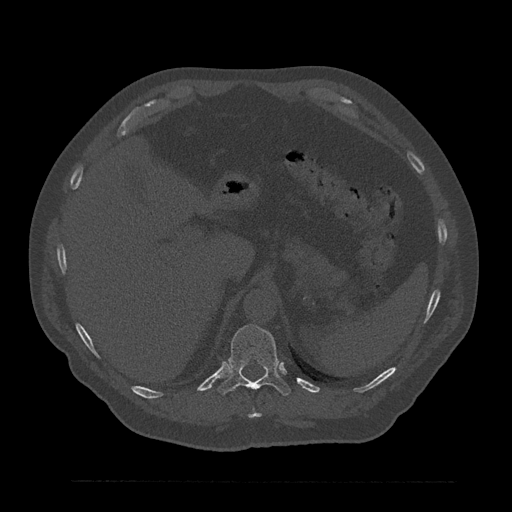
CT including the spine, one axial slice; position 301 of 797 along the scan axis; reconstruction kernel Br40s/3; 120 kVp; bone window (W 1800 / L 400 HU); 0.5 mm slice thickness; 512 × 512 image matrix, field of view 430 × 430 mm. Patient: male, 61 years. Case-level facts recorded for this patient, not image findings: primary cancer: prostate.
Structures marked on this image (semi-automatically segmented with operator editing):
- T10 vertebra: box from (x=248, y=409) to (x=261, y=418) px
- T11 vertebra: (x=218, y=325)–(x=291, y=396)